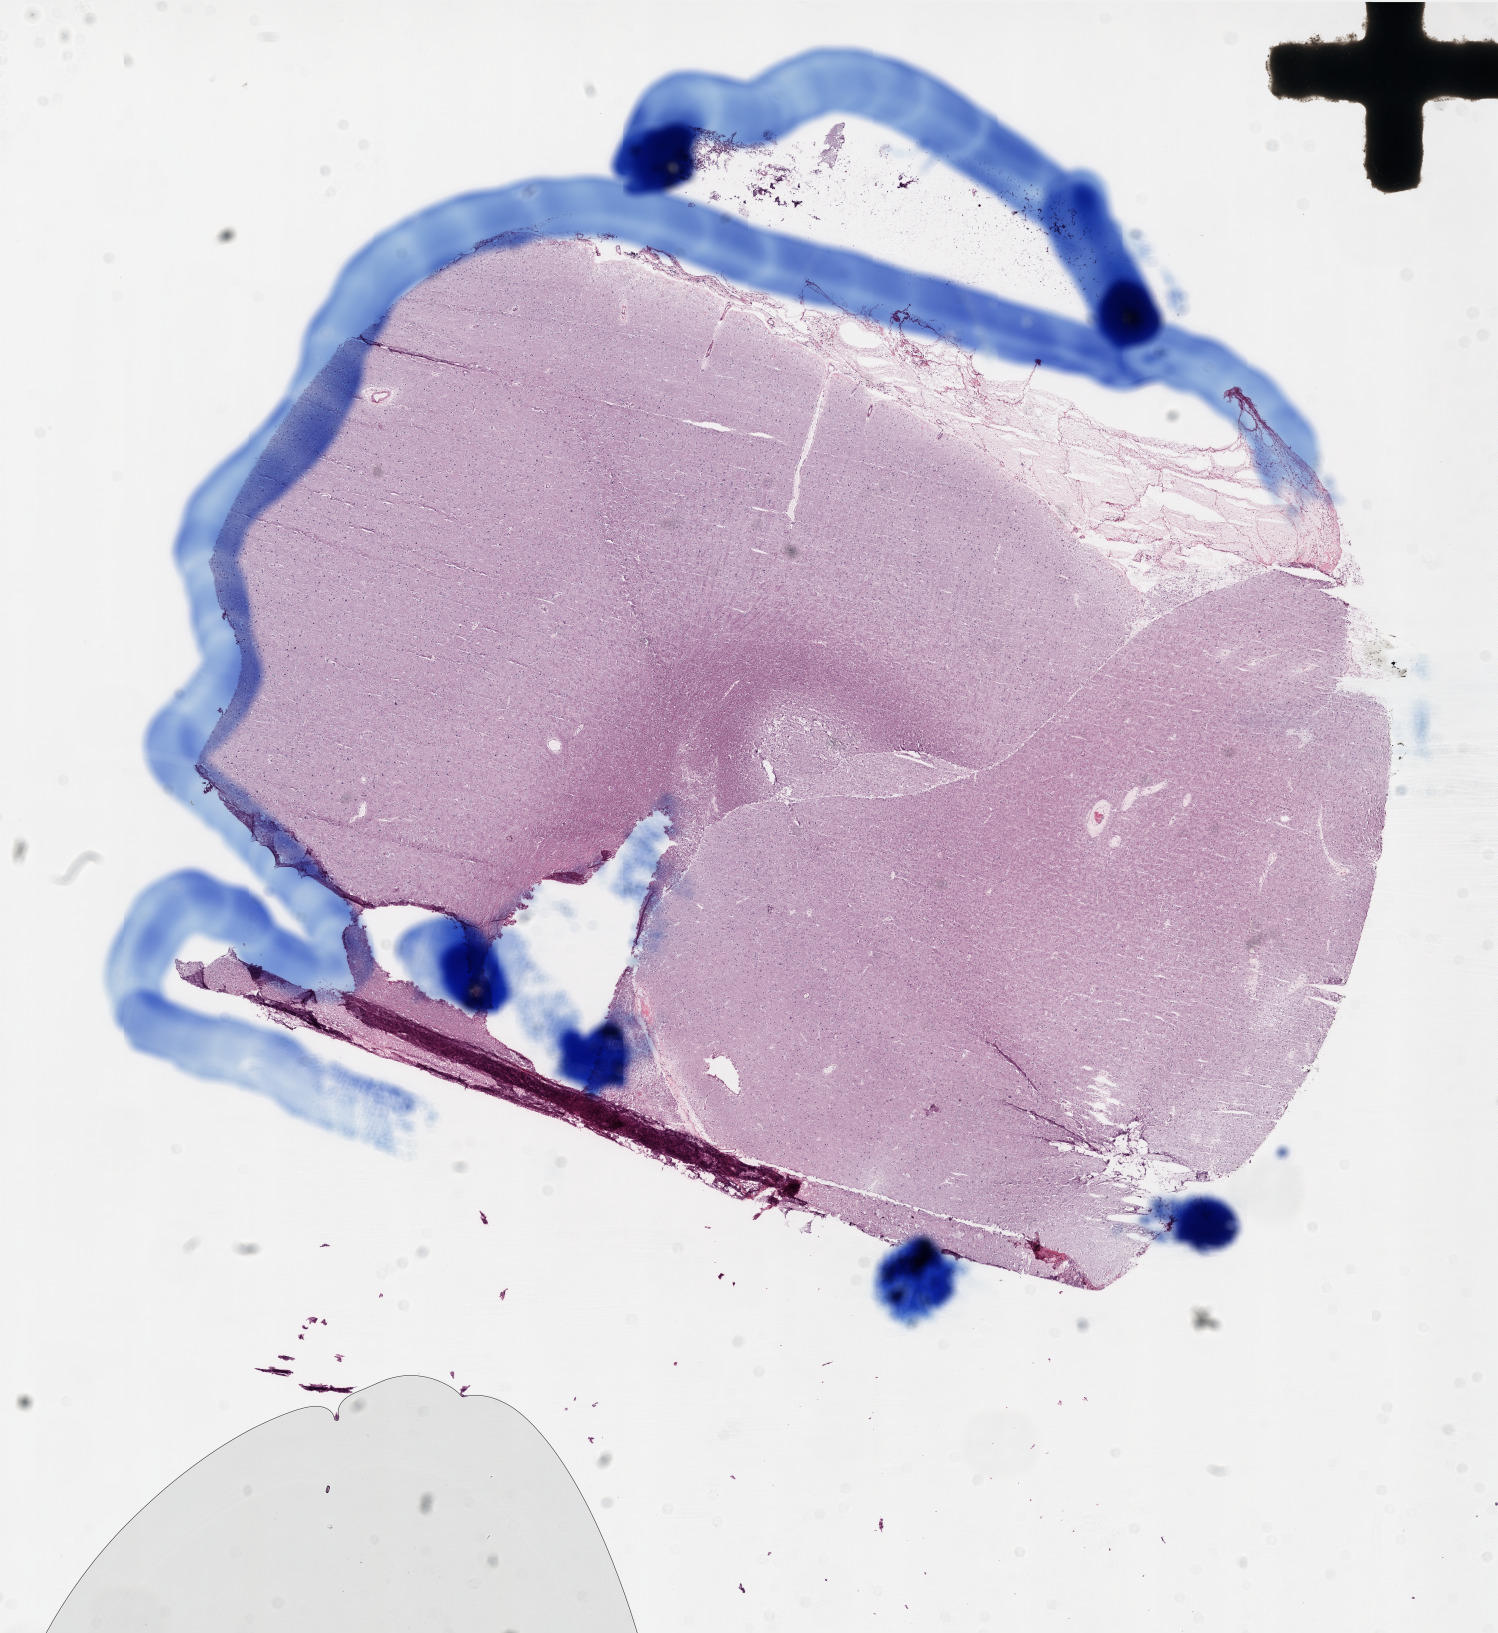
H&E whole-slide image, whole scanned area (about 12.0 x 13.1 mm, from a 20x scan) shown as a low-resolution overview; frozen section from the top of the tissue portion; primary tumour sample from the brain. Male patient; age at initial diagnosis 52 years. Slide review estimates, as recorded: tumour cells 0%, tumour nuclei 0%, normal cells 100%, stromal cells 0%, necrosis 0%.
Histologic diagnosis: Glioblastoma.